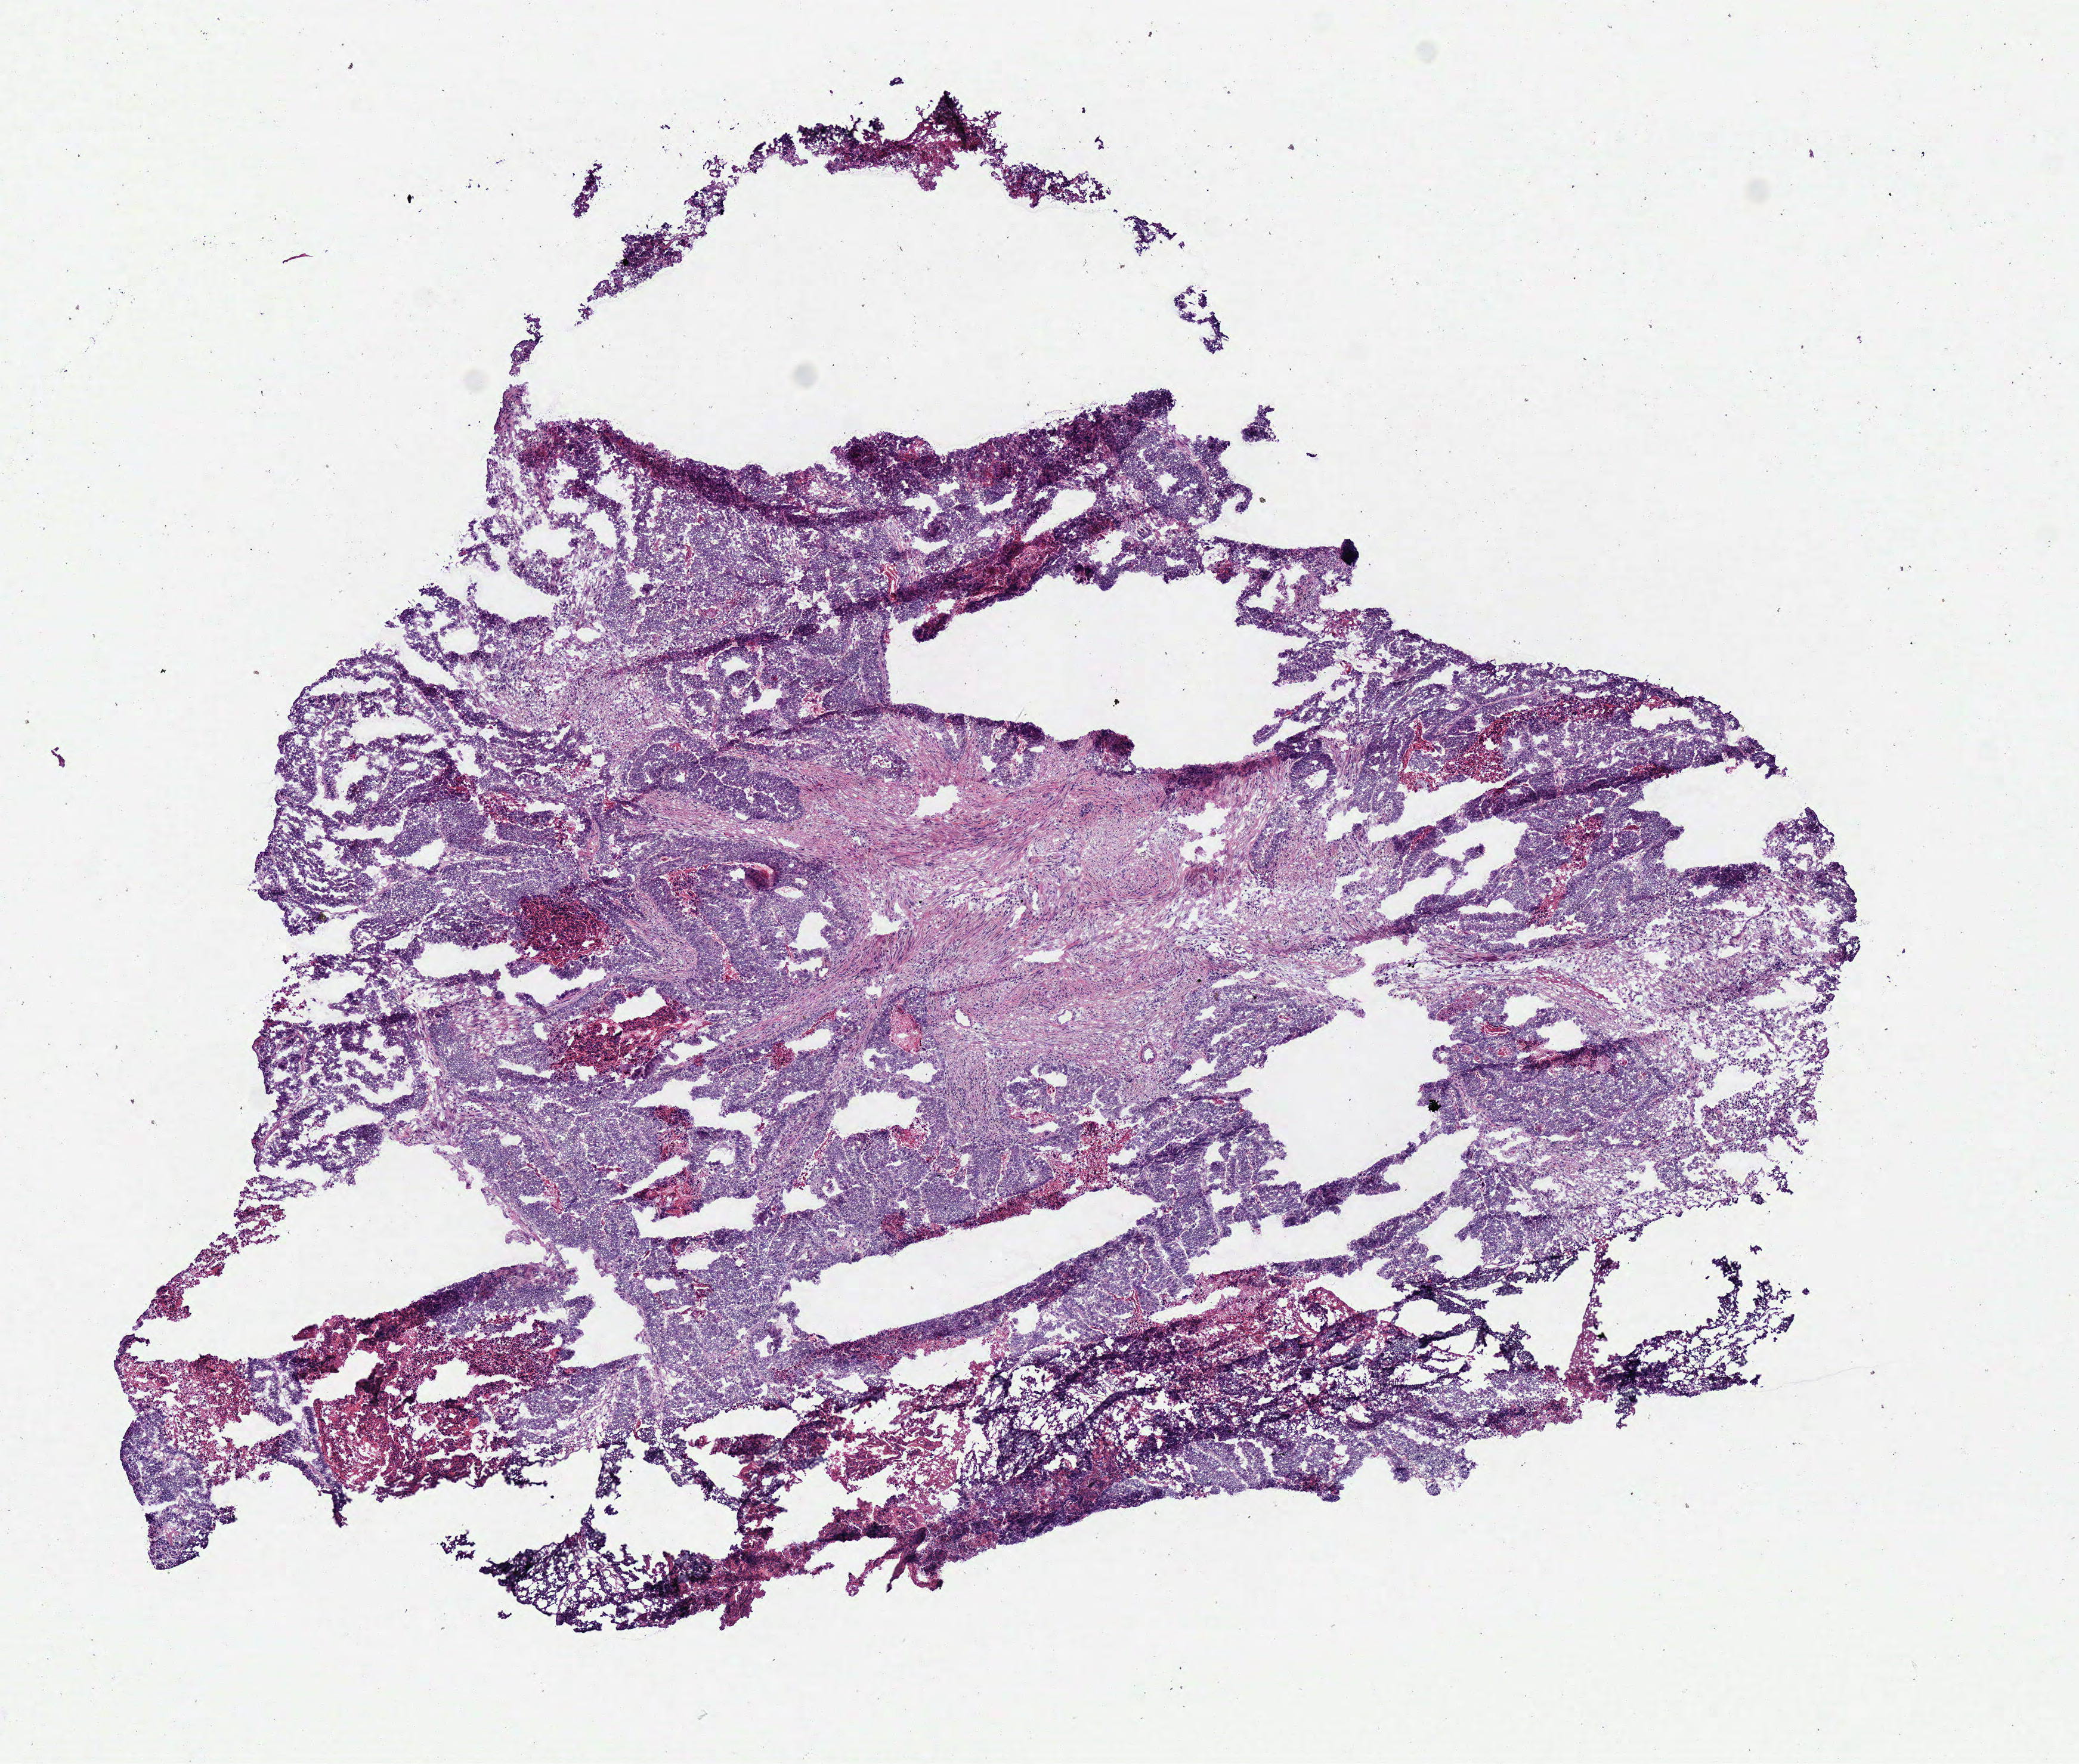
Whole-slide histology image, H&E — shown as a low-resolution overview of the whole scanned area (about 6.9 x 5.8 mm), frozen section, sample: primary tumour, rectum. Patient: male, age at initial diagnosis 59 years.
Diagnosis: Adenocarcinoma in tubulovillous adenoma.